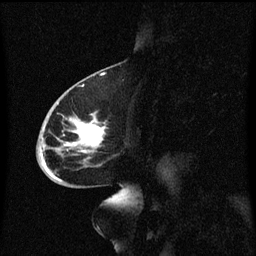
Breast MRI (dynamic contrast-enhanced), one sagittal slice. Position 32 of 60 along the scan axis. Dynamic contrast-enhanced series, image 2 of 3 at this slice position (ordered by acquisition). 1.5 T. TE 4.2 ms, TR 8.4 ms. 2 mm slice thickness. 256 × 256 image matrix. Female patient, age 68 years. From the clinical record (not read from this slice): setting: breast cancer imaged before/during neoadjuvant chemotherapy; receptor status: triple-negative.
Structures marked on this image (semi-automatically segmented with operator editing):
- analysis volume of interest (the breast-tissue region the enhancement analysis was run in; not a lesion): box from (x=37, y=94) to (x=109, y=173) px
- tumour enhancement mask (voxels above the 70 % enhancement threshold inside the analysis volume of interest): (x=42, y=116)–(x=106, y=173)